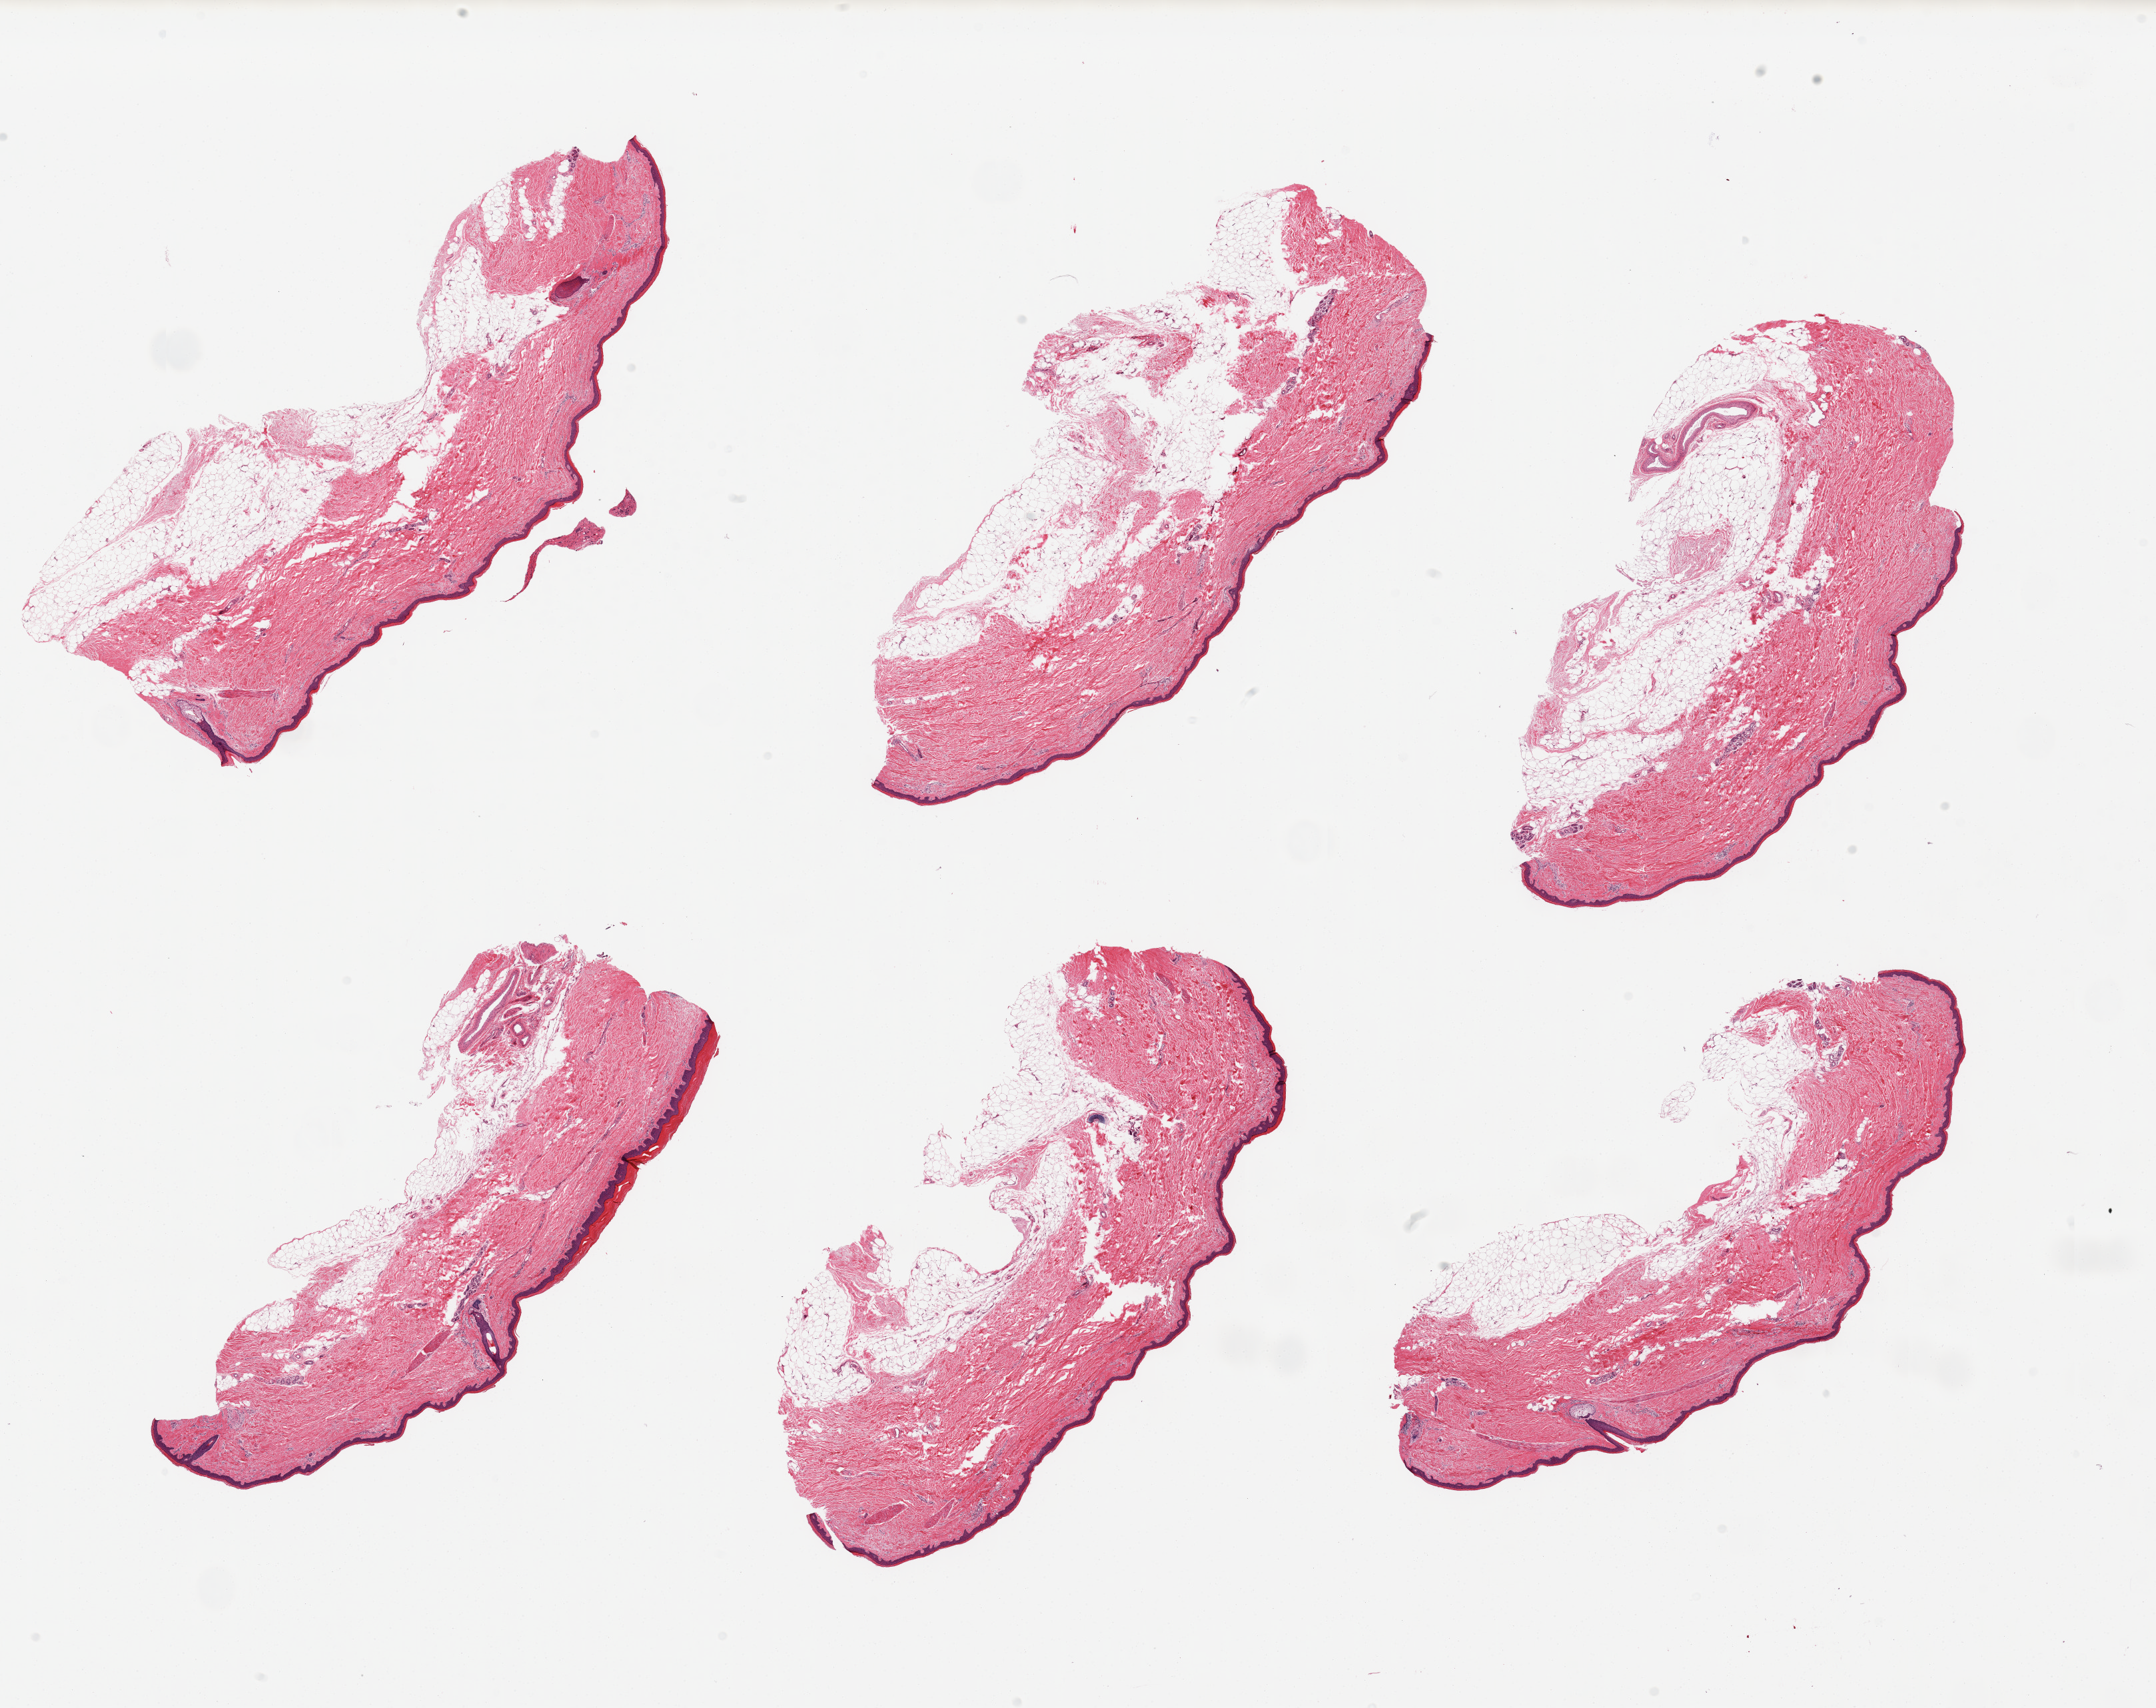
Whole-slide image, haematoxylin and eosin stain, brightfield, whole scanned area (about 25.6 x 20.3 mm) shown as a low-resolution overview, PAXgene-fixed, paraffin-embedded tissue, sampled site (target tissue): skin of lower leg, tissue donor sample. Donor: male.
Review note (as recorded): 6 pieces; each piece contains external fat up to 2.6 mm thick; epidermis measures 42.9 um in thickness.